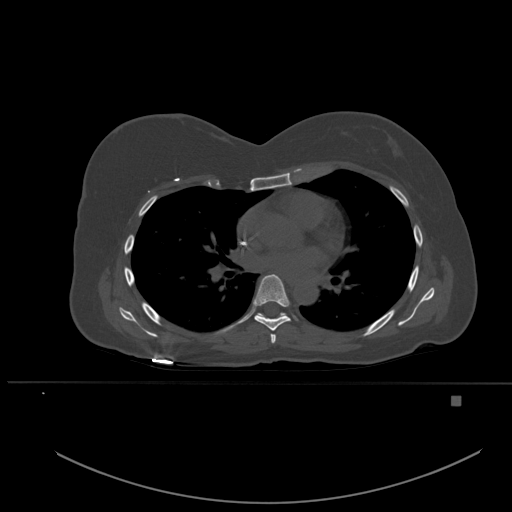
CT including the spine, one axial slice; position 348 of 651 along the scan axis; bone window (W 1800 / L 400 HU); 1.5 mm slice thickness; 512 × 512 image matrix, field of view 443 × 443 mm. Patient: female, 49 years. Case-level facts recorded for this patient, not image findings: primary cancer: breast; vertebrae with lytic lesions (as recorded): L3, T12, L4.
Outlined on this slice (semi-automatically segmented with operator editing):
- T5 vertebra: box from (x=270, y=334) to (x=276, y=343) px
- T6 vertebra: (x=254, y=274)–(x=291, y=331)
- T7 vertebra: (x=257, y=312)–(x=287, y=316)